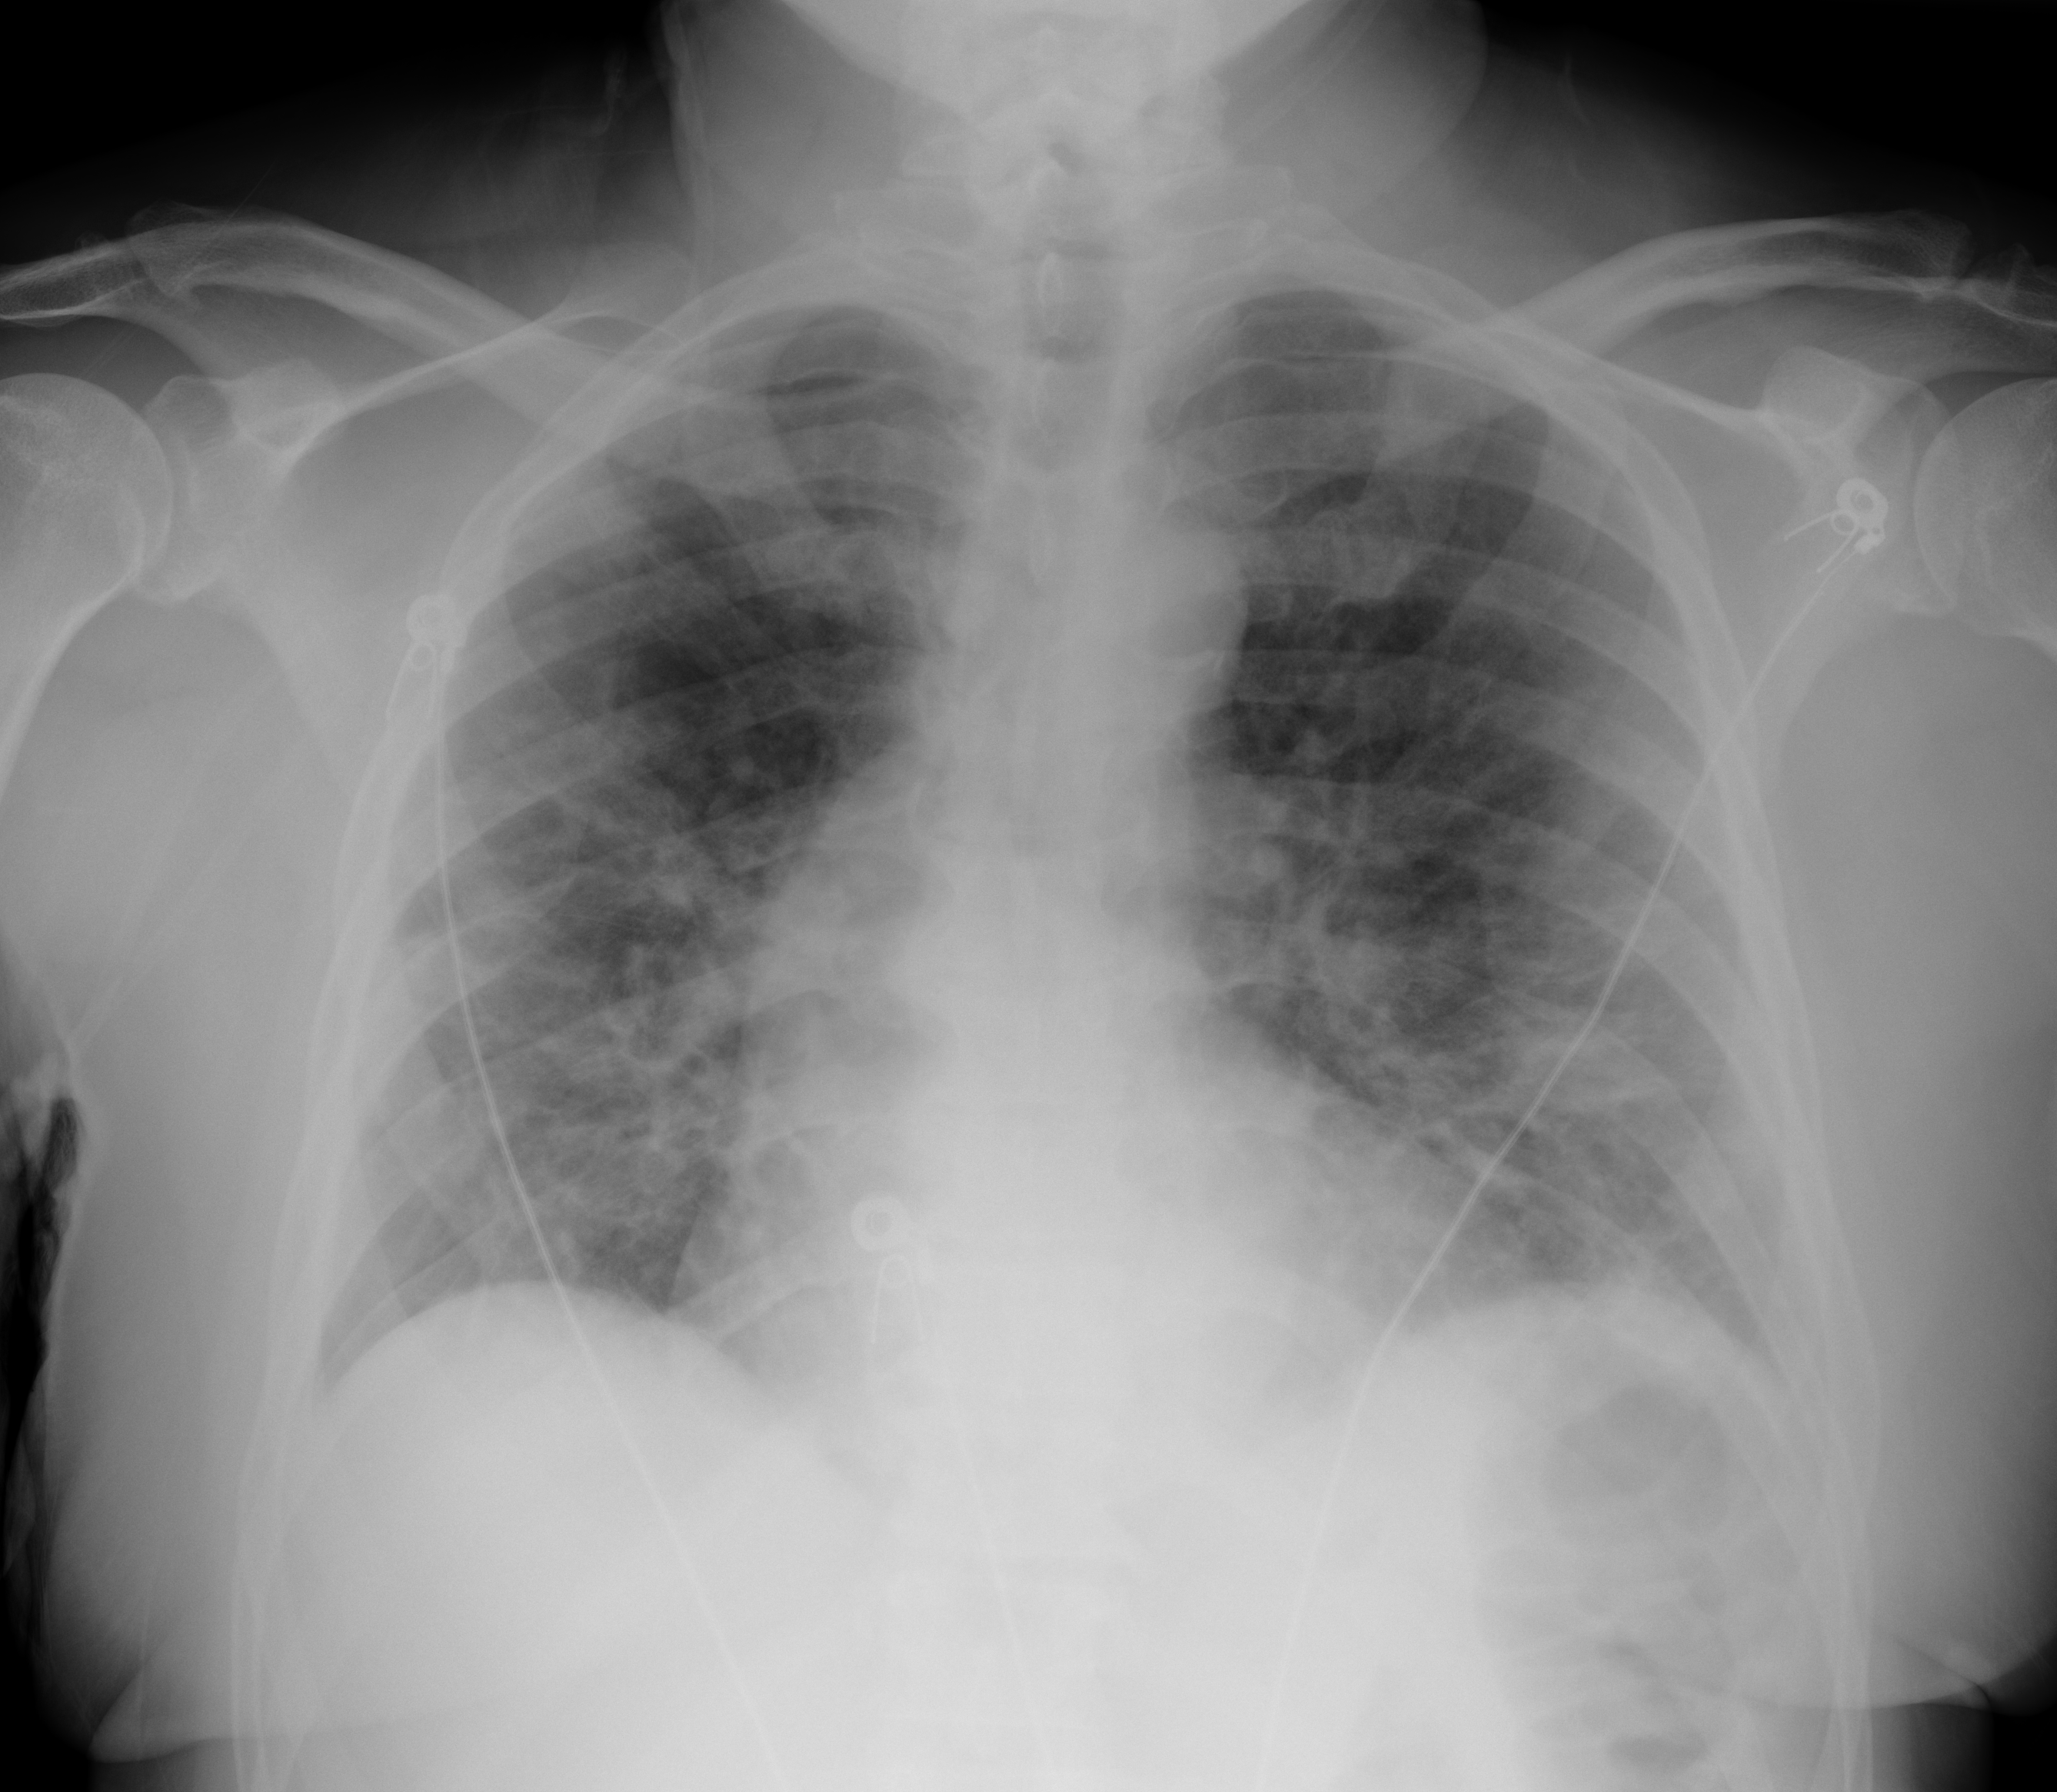
Portable chest radiograph, AP projection. Male patient, age 64 years; imaged 0 days after the COVID-19 diagnosis.
Key findings recorded by the radiologist: Subtle perihilar hazy opacity noted bilaterally consistent with early airspace disease but no dense consolidation.